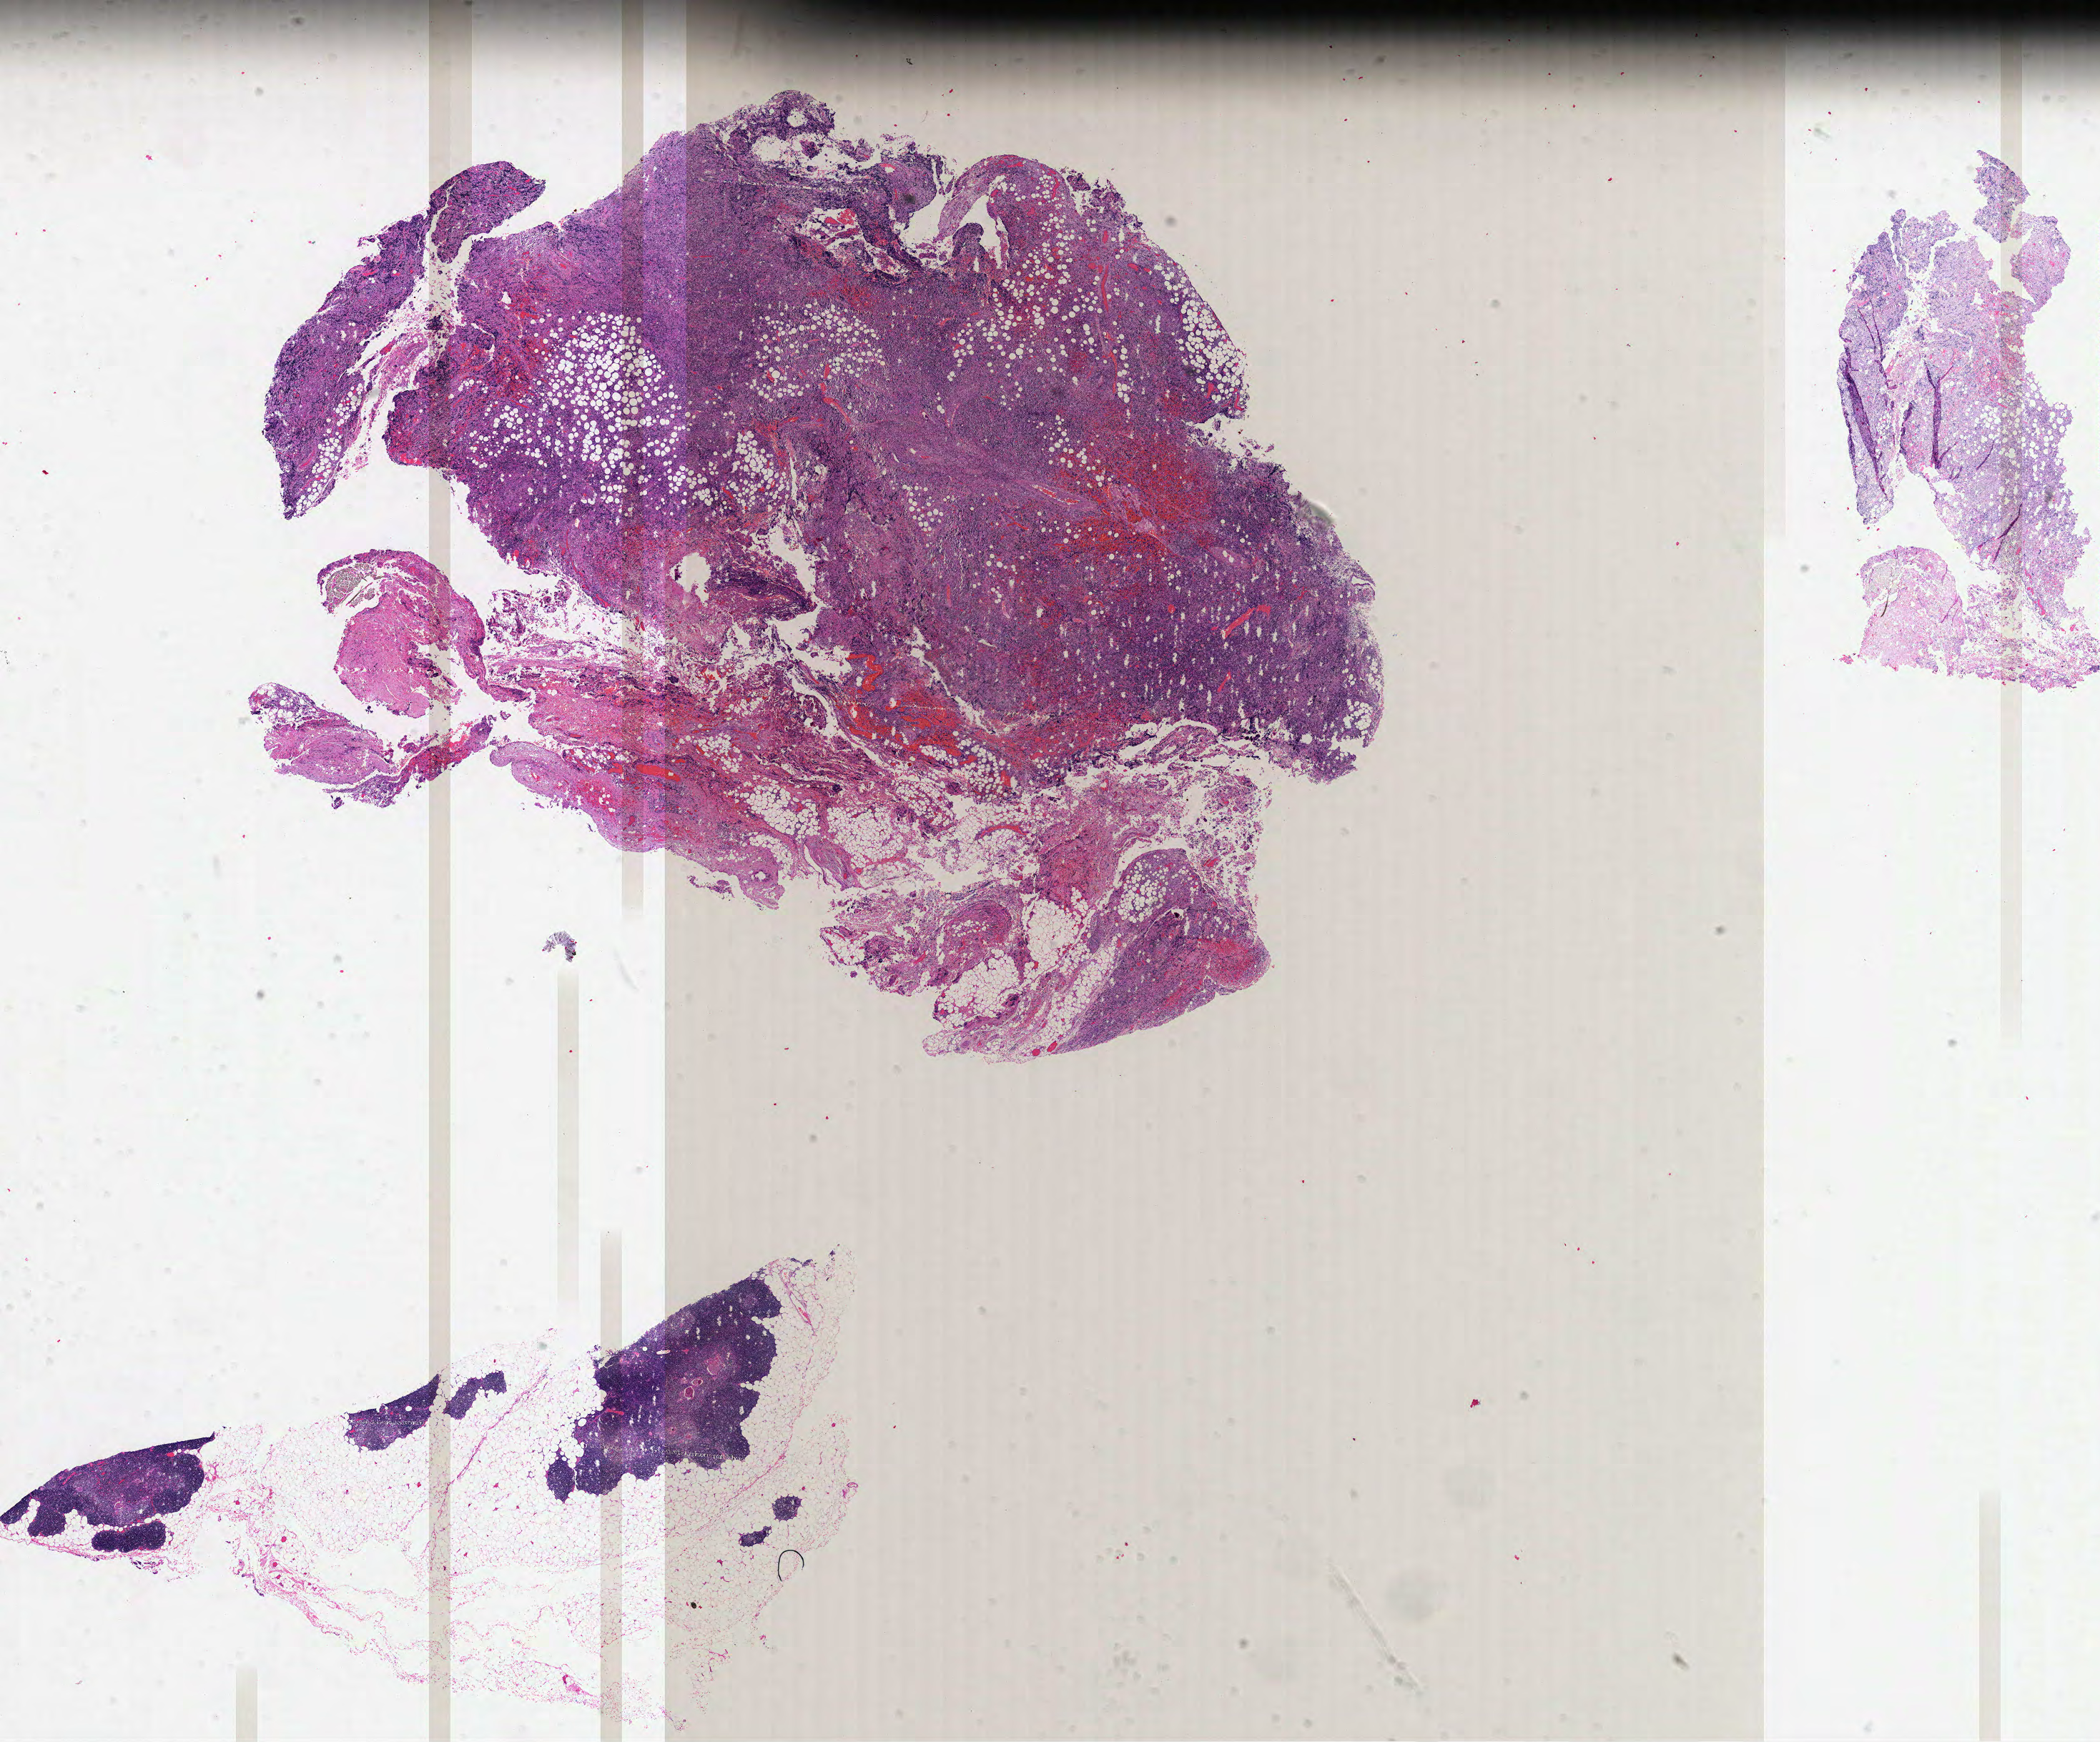
Digitized H&E tissue section (whole slide), low-resolution overview of the scanned area, about 23.7 x 19.7 mm (acquisition: 40x scan); FFPE section; sample: primary tumour, lymphoid tissue. Patient: male, age at initial diagnosis 51 years.
* diagnosis: Diffuse large B-cell lymphoma, NOS